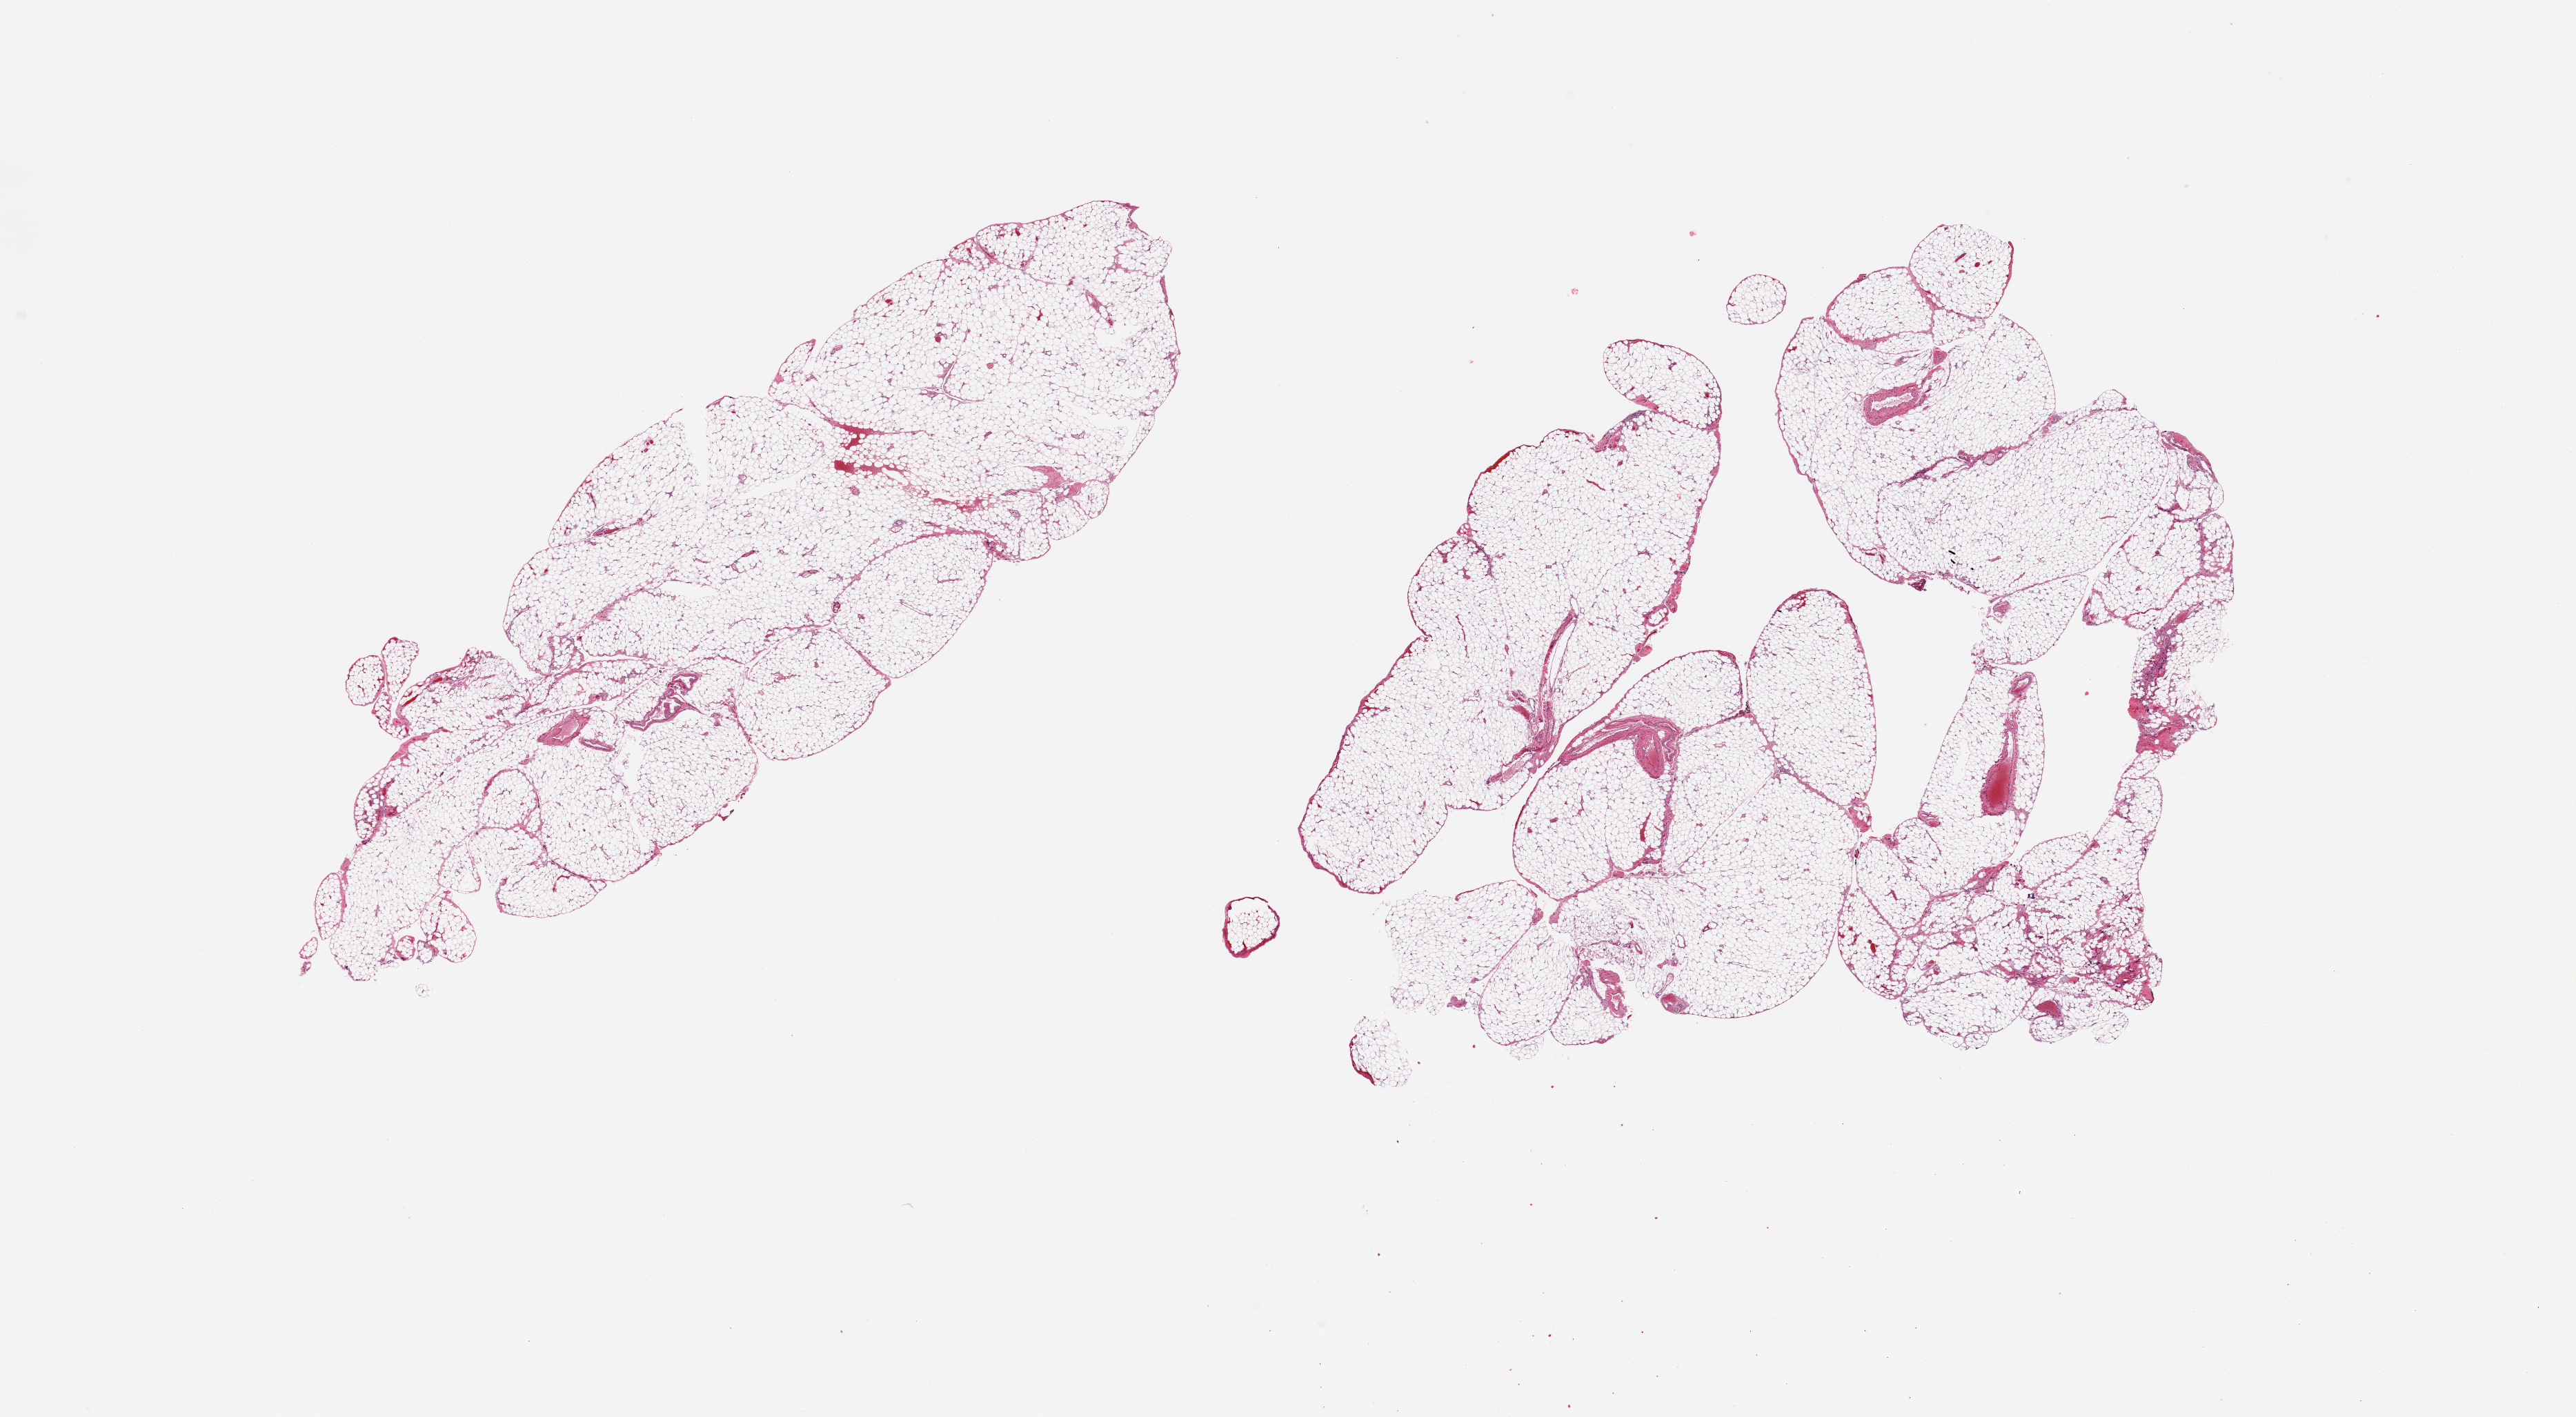
Digitized haematoxylin and eosin-stained section — shown as a low-resolution overview of the whole scanned area (about 29.5 x 16.2 mm, acquisition: 20x scan). PAXgene-fixed, paraffin-embedded tissue. Sampled site (target tissue): omentum. Donor tissue sample. Donor: male.
Pathologist's review note for this sample: 2 pieces; <5% fibrovascular component.